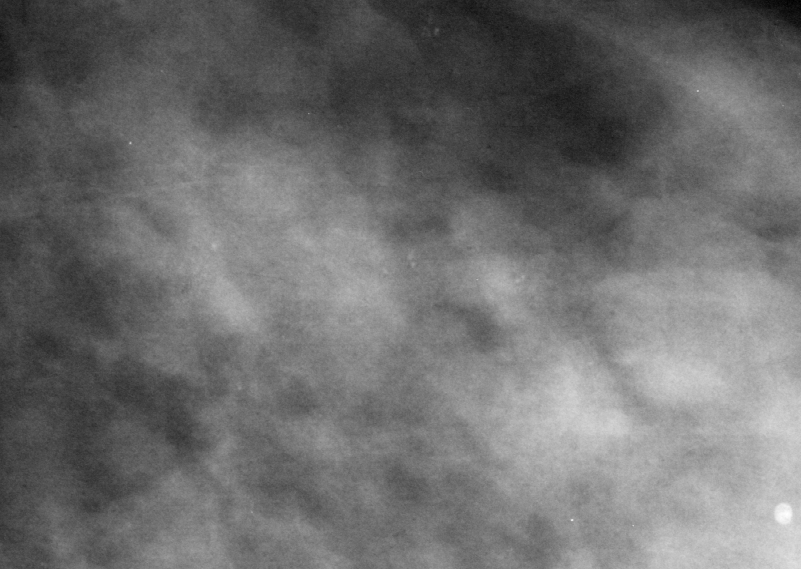
Crop from a digitized film mammogram around one marked abnormality; left breast; MLO view; BI-RADS breast density category 4 (scale 1–4).
Marked abnormality: calcifications, morphology amorphous, distribution segmental; BI-RADS assessment category 4; pathology result (as recorded, not read from the image): benign.